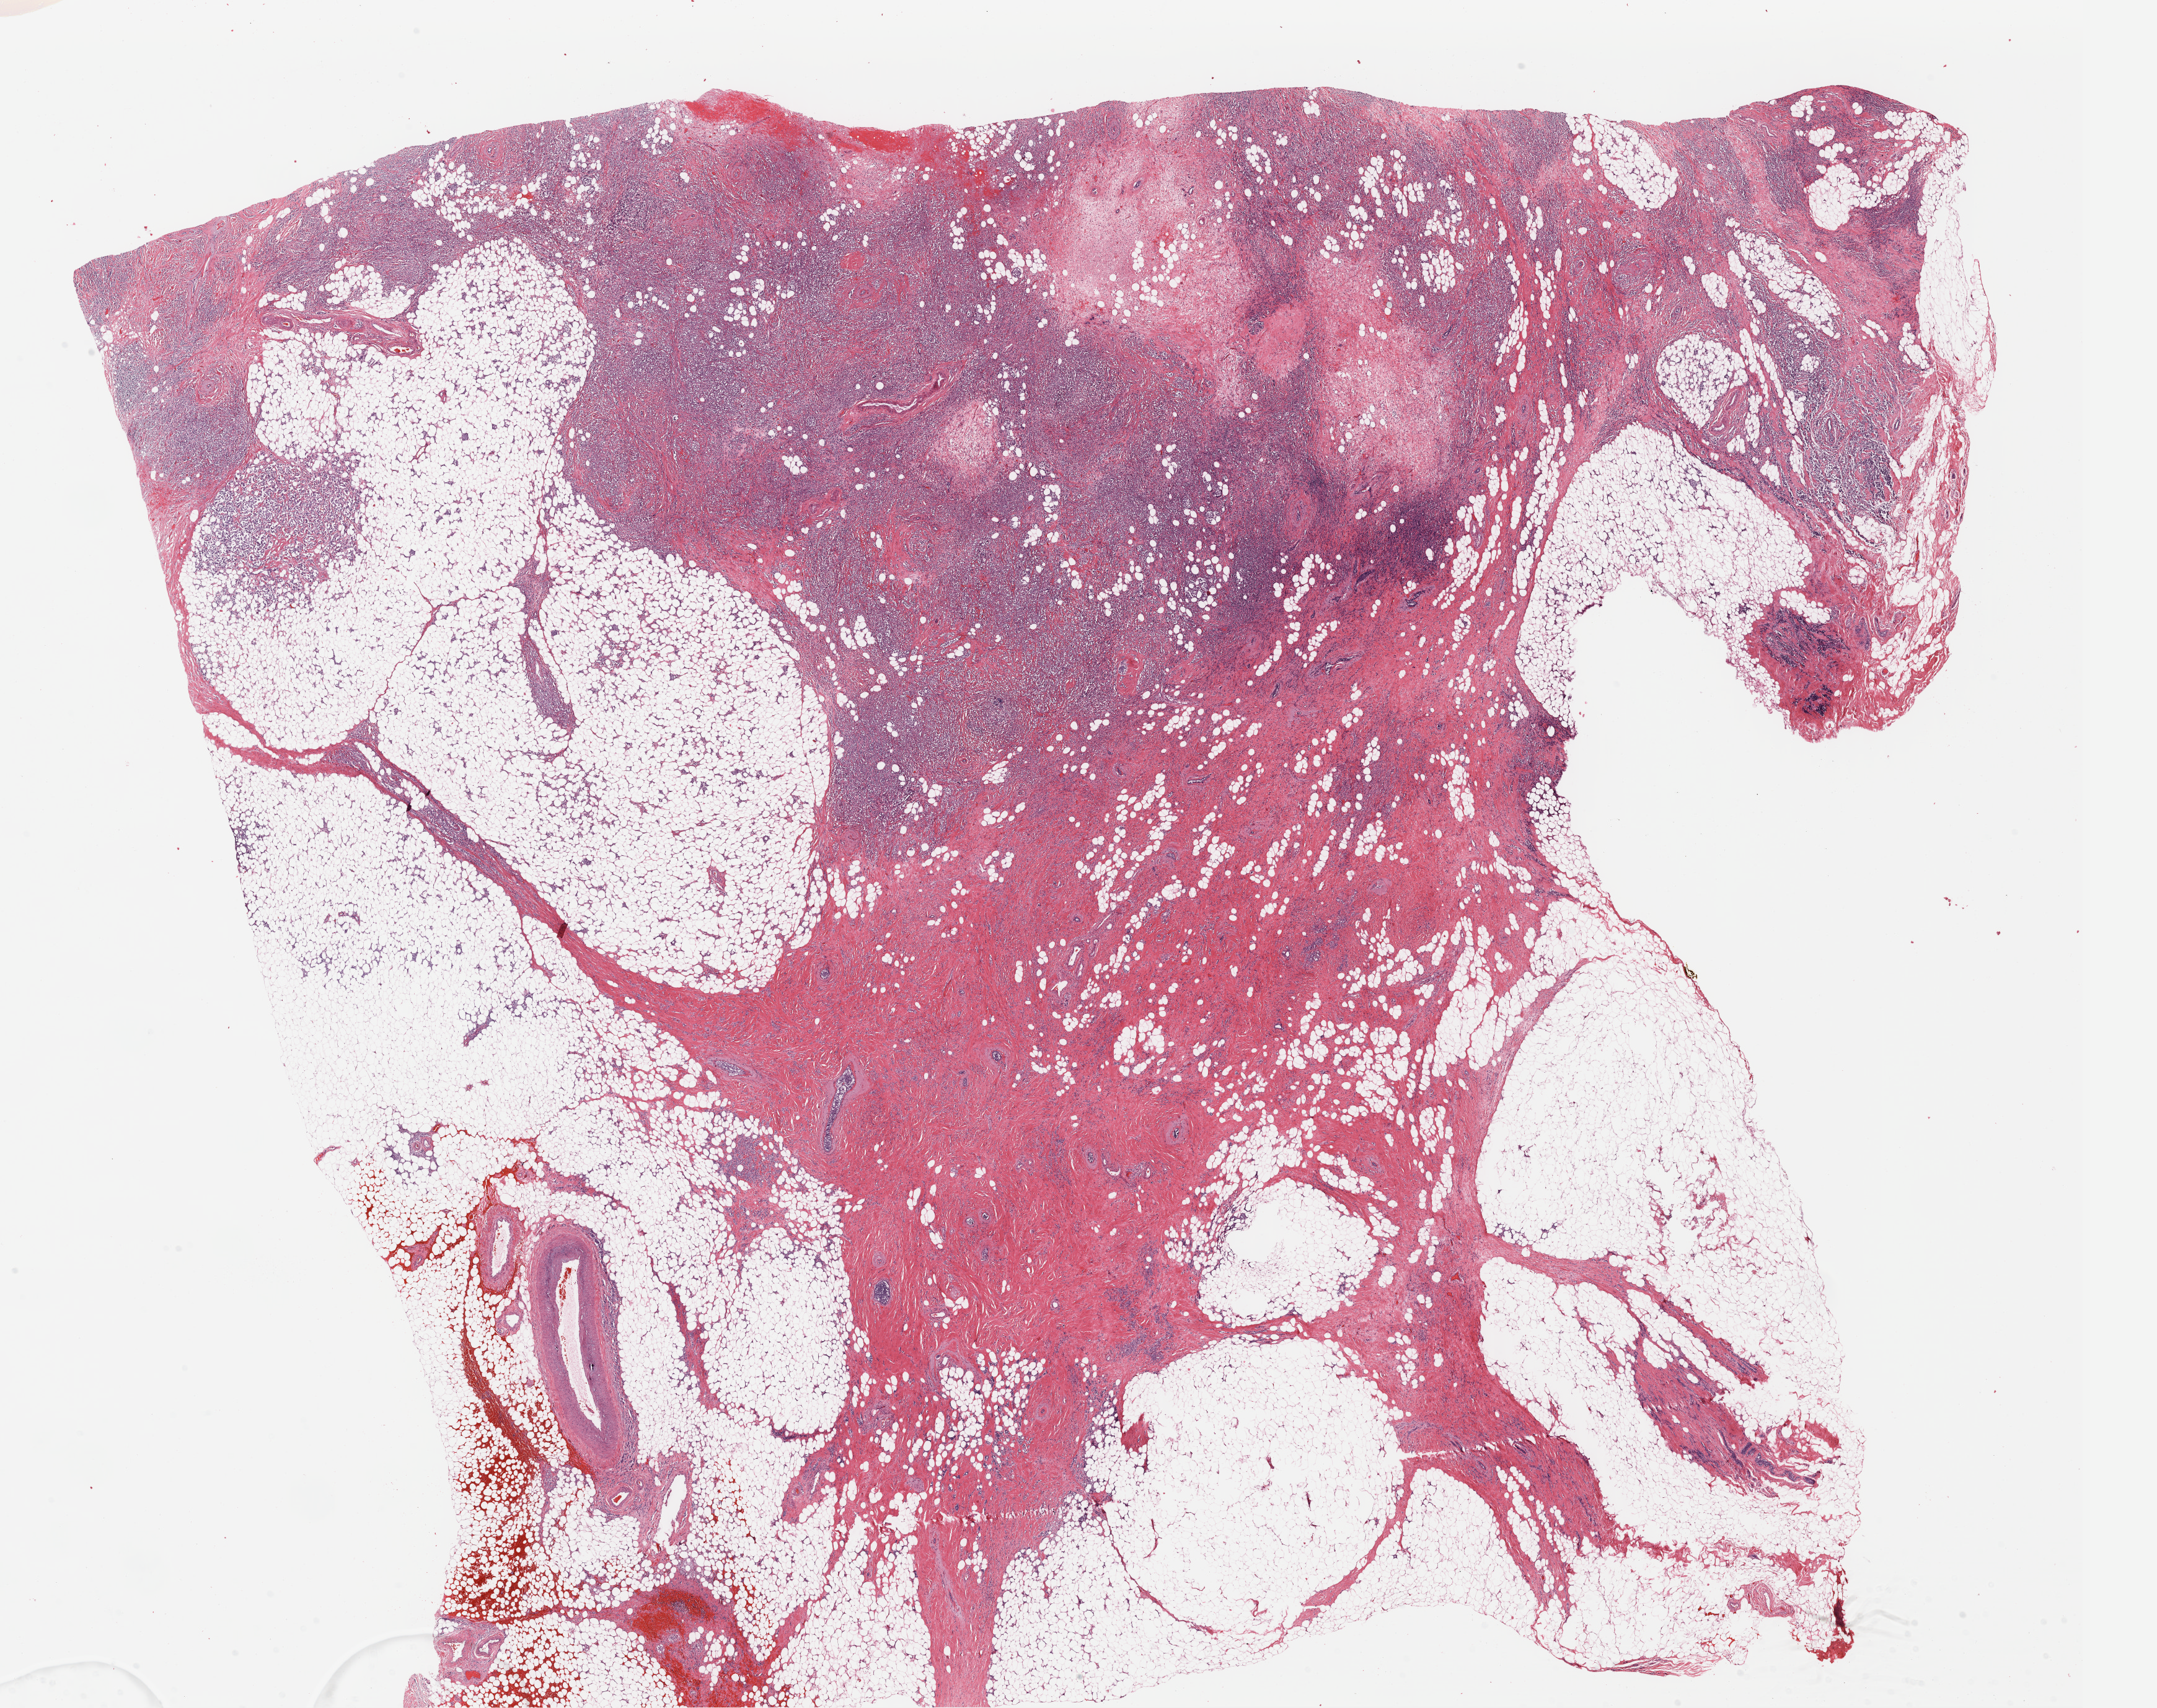
Hematoxylin and eosin (H&E) stained whole-slide image — a low-resolution overview of the entire scanned area, about 27.4 x 21.7 mm. Formalin-fixed paraffin-embedded (FFPE) diagnostic section. Sample: primary tumour, breast. Patient: female, age at initial diagnosis 73 years.
• diagnosis: Lobular carcinoma, NOS
• lymph nodes positive (case pathology): 3 of 26 examined
• AJCC pathologic stage: IIIA (7th edition)